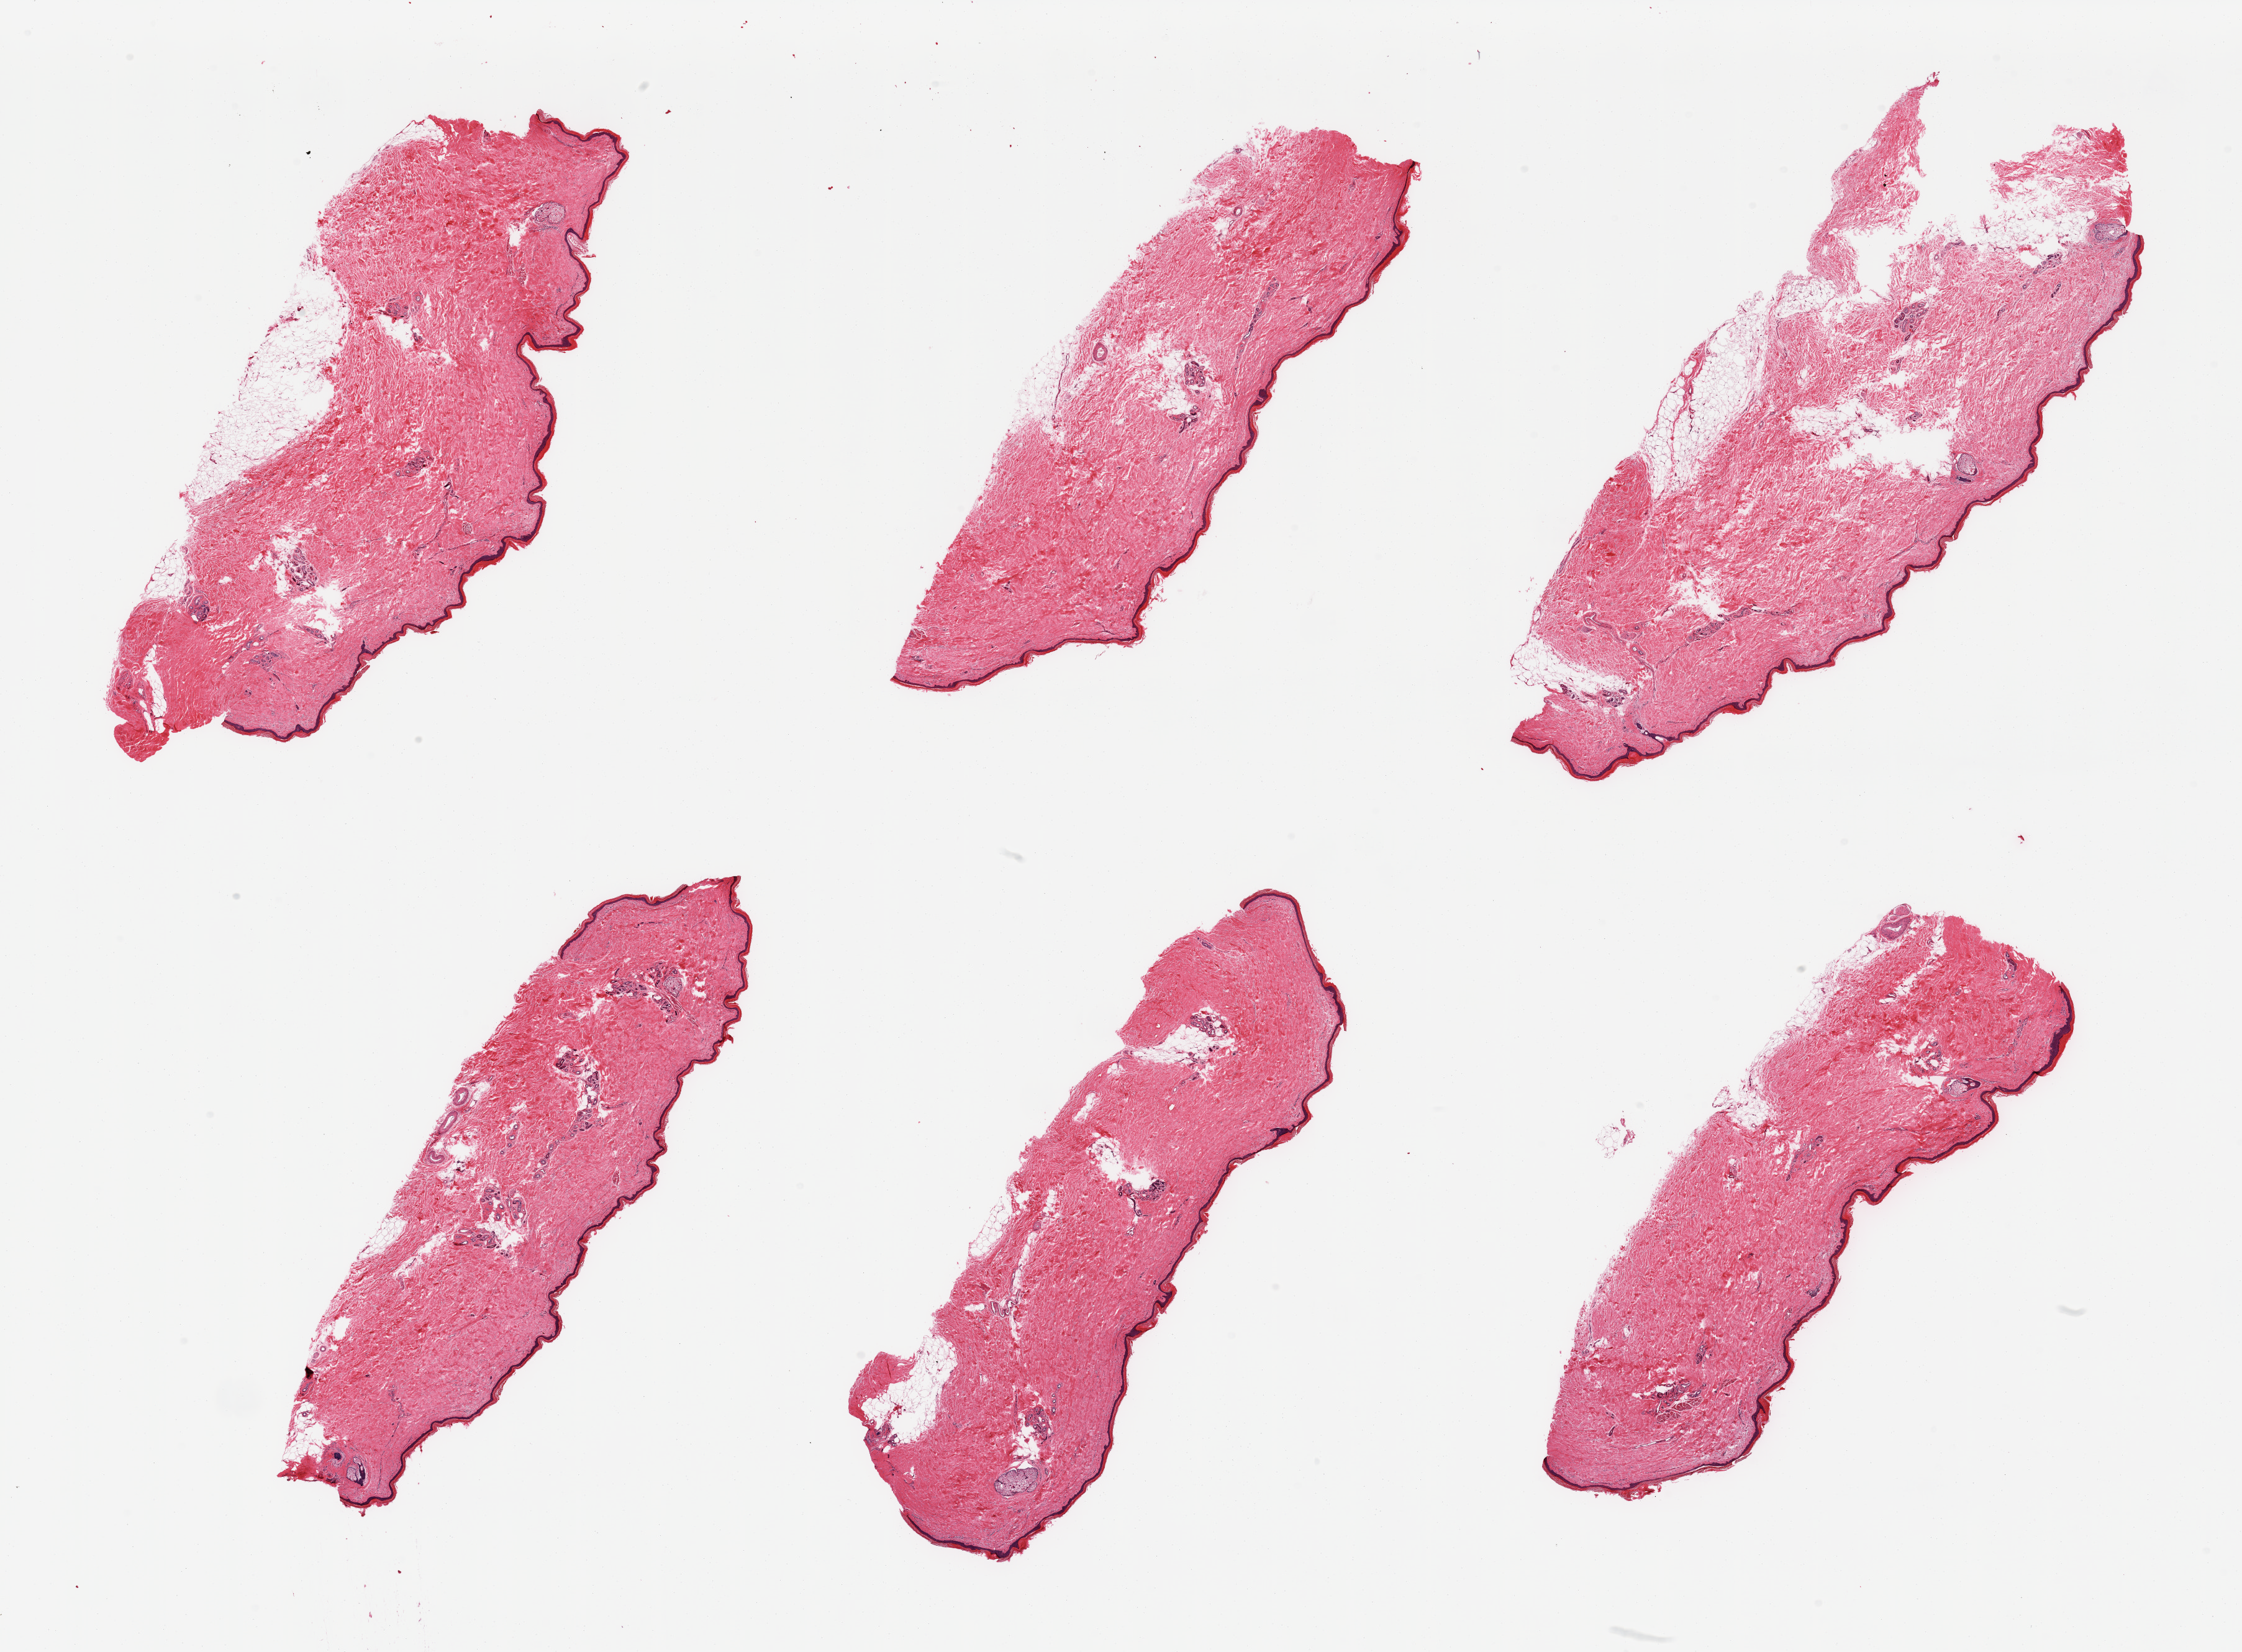
Haematoxylin and eosin whole-slide image, brightfield — a low-resolution overview of the entire scanned area, about 28.5 x 21.0 mm (acquisition: 20x scan); PAXgene-fixed paraffin-embedded (PFPE) section; sampled site (target tissue): skin of lower leg; tissue donor sample. Donor: male.
Reviewer comment on this tissue sample: 6 pieces; up to 1 mm subcutaneous fat in 2 of 6 pieces; up to 10% dermal fat.